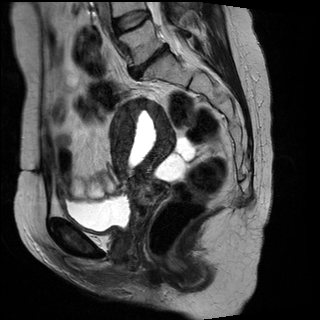
Pelvic MRI for cervical cancer, one sagittal slice. Position 14 of 29 along the scan axis. T2-weighted. 1.5 T. TE 89 ms, TR 2930 ms. 4 mm slice thickness. 320 × 320 image matrix, field of view 260 × 260 mm. Patient: female, 45 years.
Structures marked on this image (expert manual segmentation):
- uterus and cervix: bounding box (x1, y1, x2, y2) in pixels: (109, 99, 175, 213)